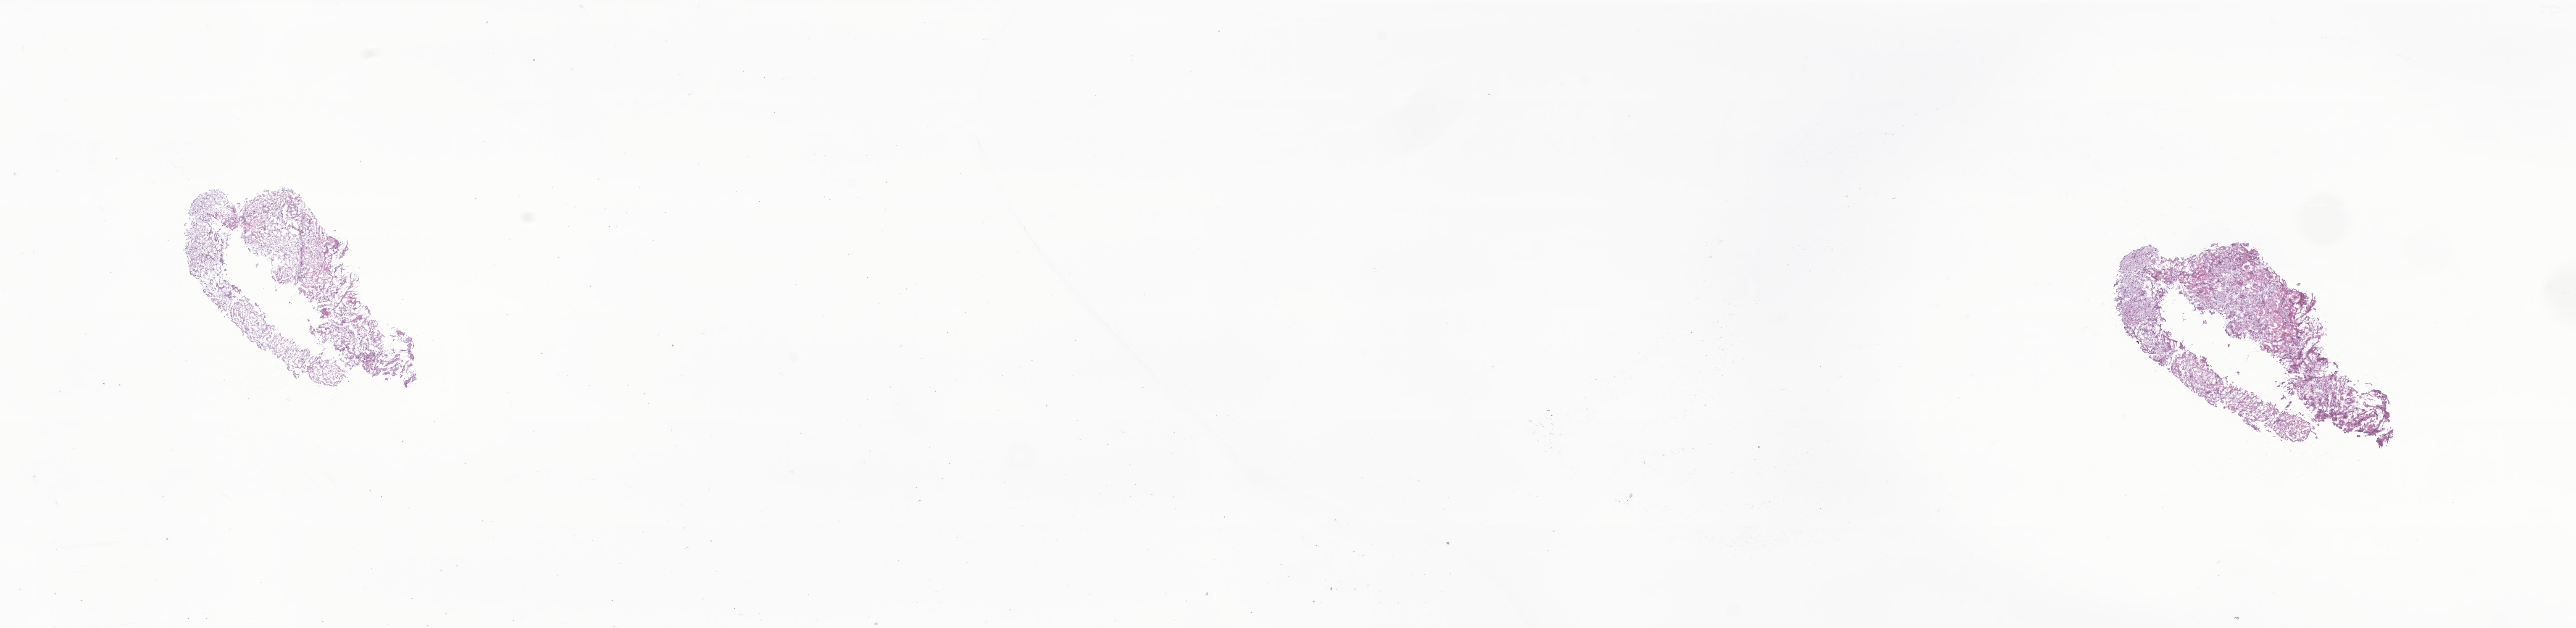
Haematoxylin and eosin whole-slide image of tumor tissue from the brain stem, whole scanned area (about 25.8 x 6.3 mm) shown as a low-resolution overview; frozen section (OCT-embedded). Patient female; age 50 months (4 years 2 months).
• diagnosis: Pilocytic astrocytoma